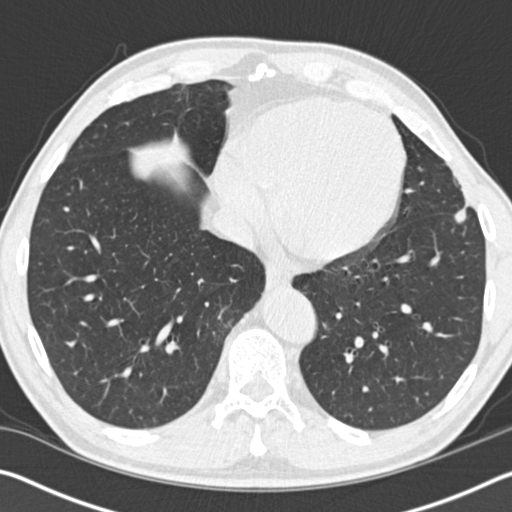
Low-dose screening chest CT, one axial slice. Slice 46 of 162 in the series (ordered by position). Reconstruction kernel B30f. 120 kVp. Lung window (W 1500 / L -600 HU). 2 mm slice thickness. 512 × 512 image matrix, field of view 340 × 340 mm.
Structures marked on this image (expert manual segmentation):
- lesion 1 (tumor, upper lobe of left lung): bounding box [x1, y1, x2, y2] px = [454, 202, 471, 223]